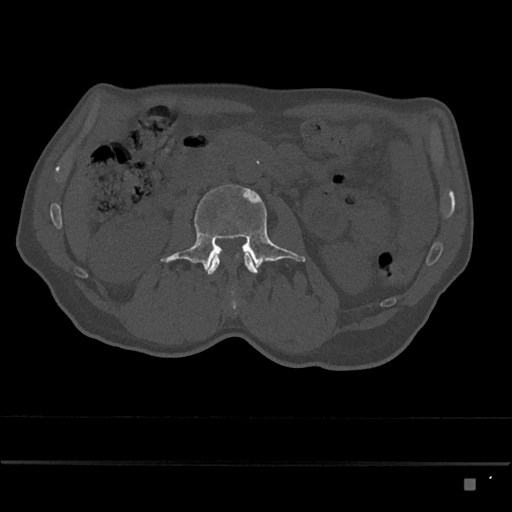
CT including the spine, one axial slice; position 425 of 797 along the scan axis; 120 kVp; bone window (W 1800 / L 400 HU); 0.5 mm slice thickness; 512 × 512 image matrix, field of view 390 × 390 mm. Patient: male, 72 years. From the clinical record (not read from this slice): primary cancer: prostate.
Structures marked on this image (semi-automatic segmentation, software-assisted and operator-edited):
- L2 vertebra: bounding box (x1, y1, x2, y2) in pixels: (205, 253, 258, 275)
- L3 vertebra: (161, 184, 306, 294)